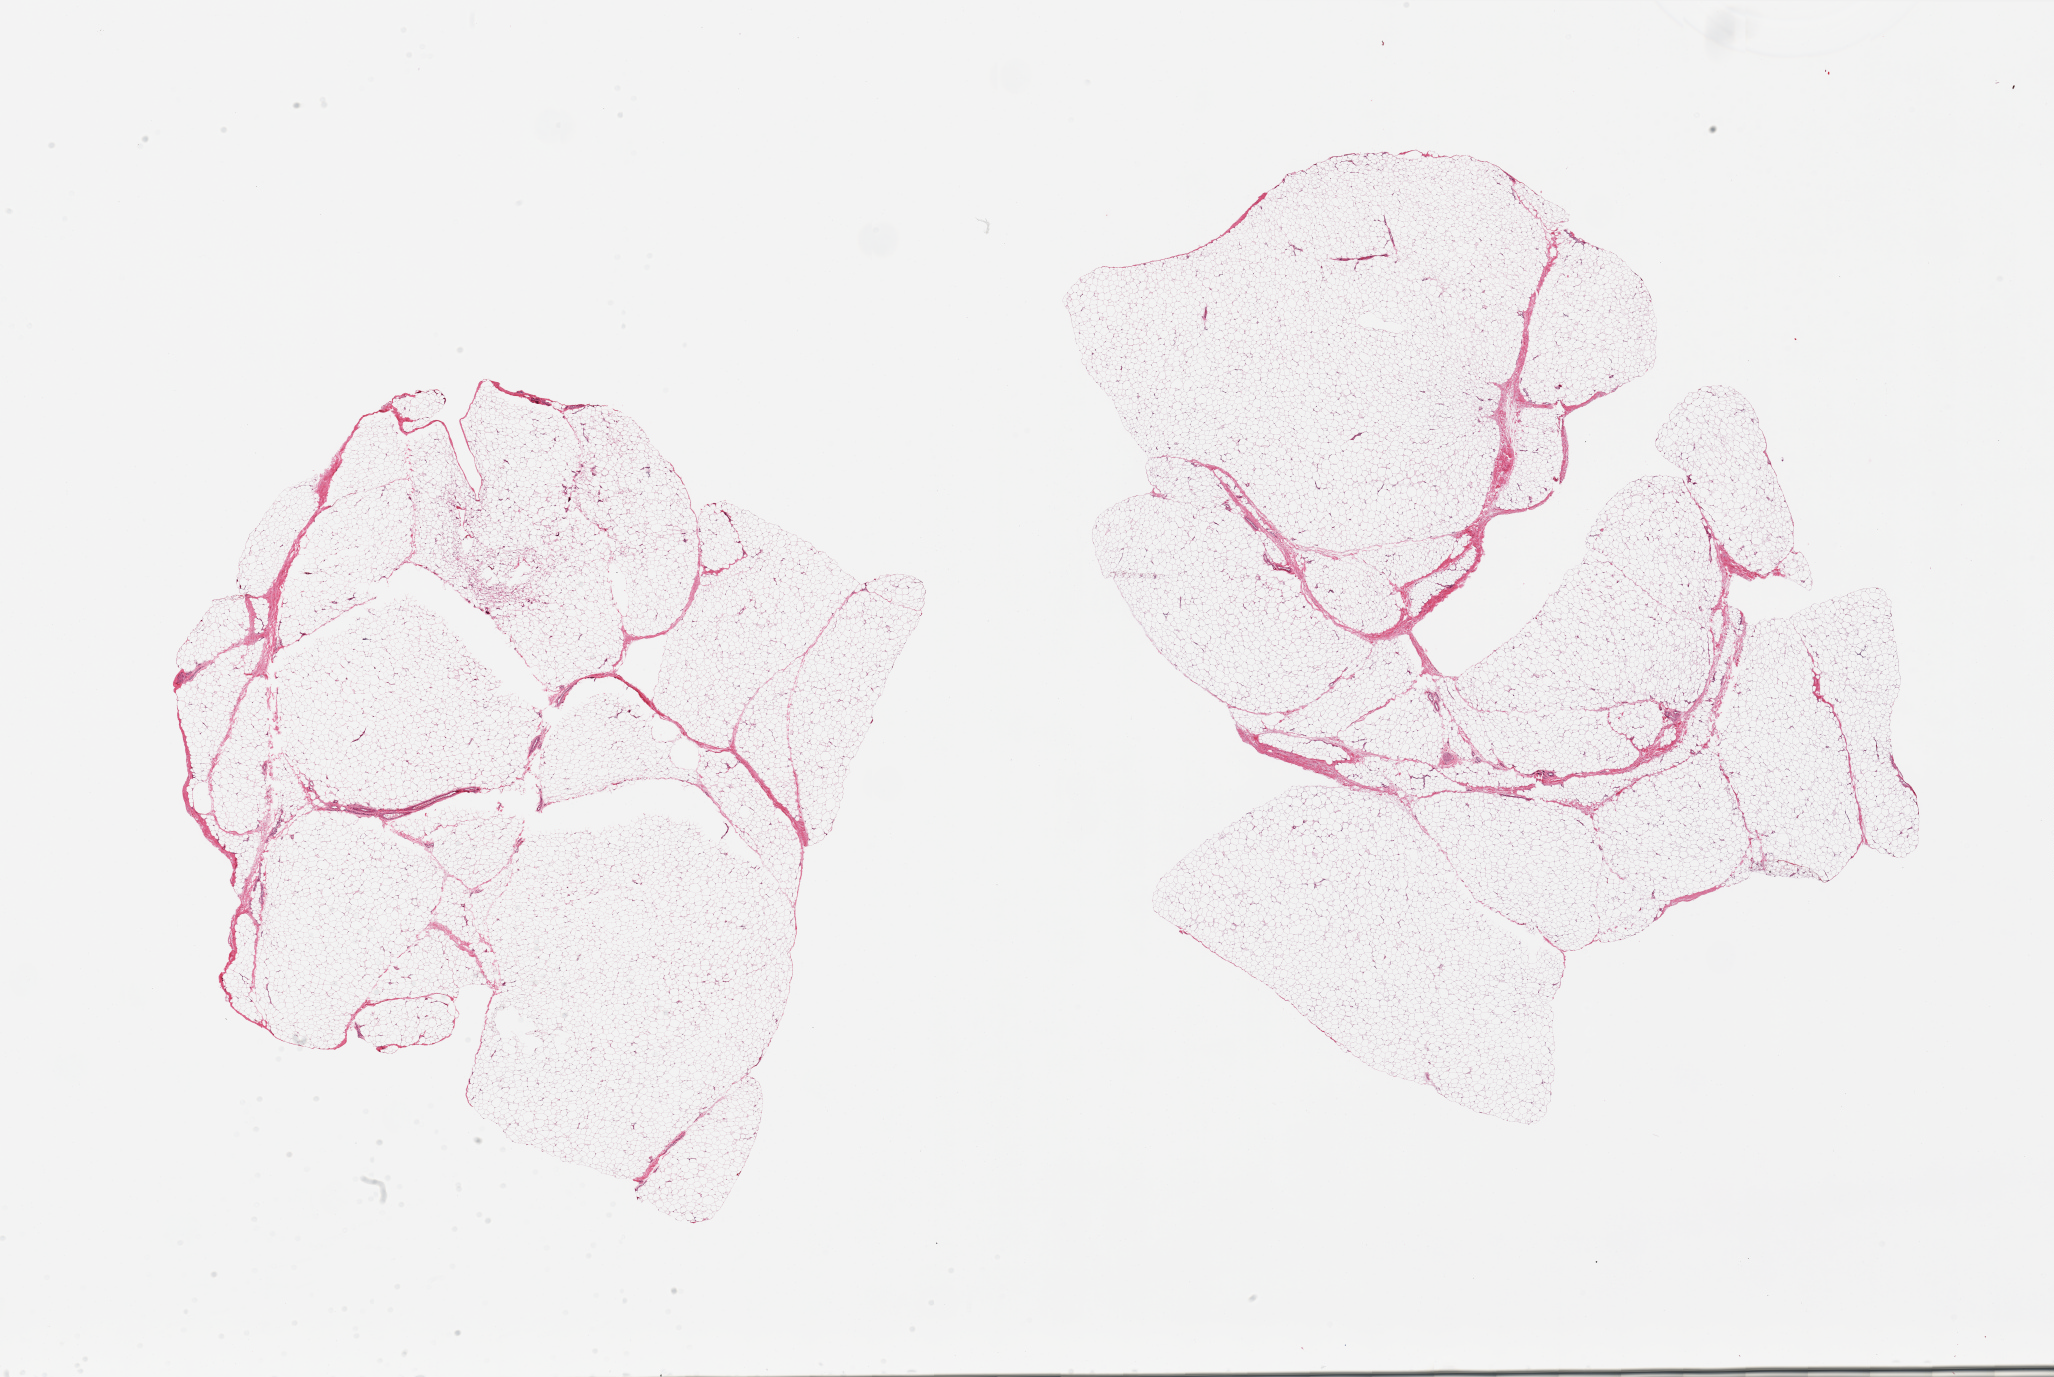
Haematoxylin and eosin whole-slide image, shown as a low-resolution overview of the whole scanned area (about 32.5 x 21.8 mm, slide scanned at 20x), PAXgene-fixed, paraffin-embedded tissue, target tissue: adipose tissue, tissue donor sample. Donor sex: male.
Review note (as recorded): 2 pieces, trace fascia.